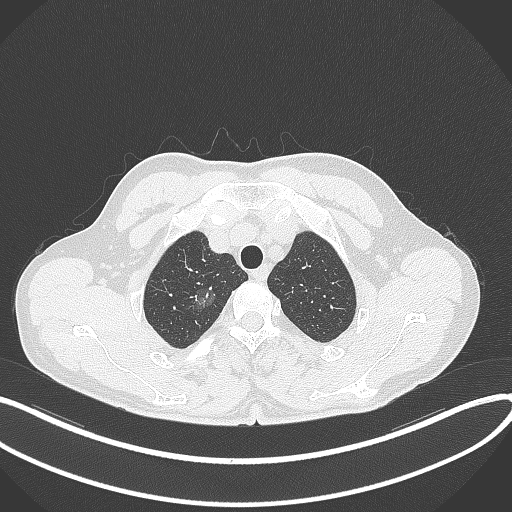
Chest CT, one axial slice. Slice 328 of 407 in the series (ordered by position). 120 kVp. Lung window (W 1500 / L -600 HU). 512 × 512 image matrix. Patient: male, 58 years. From the clinical record (not read from this slice): clinical TNM (as recorded): T1c N0 M0.
Annotated regions visible in this slice (rectangle marked by the reading radiologist):
- lung tumour (recorded histology: adenocarcinoma): bounding box (x1, y1, x2, y2) in pixels: (190, 278, 220, 310)